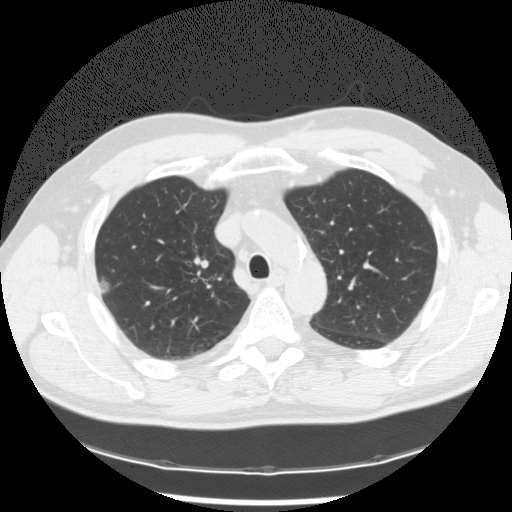
Axial slice from a low-dose chest CT screening exam. First (baseline) screen. Lung window (W 1500 / L -600 HU). 120 kVp. 512 × 512 image matrix. Male, age 62 years at enrolment. Former smoker at enrolment.
Expert reader's lesion annotation, bounding box [x1, y1, x2, y2] px = [88, 271, 116, 301]. The exam's reader record, not a measurement of the box and not confirmed to be the same lesion: non-calcified nodule or mass ≥4 mm, right upper lobe, 14 × 11 mm, poorly defined margins, mixed attenuation. Official screen result: positive, change unspecified: nodule(s) >= 4 mm or enlarging nodule(s), mass(es), or other non-specific abnormalities suspicious for lung cancer. Later outcome: lung cancer diagnosed 343 days after this screen — adenocarcinoma, NOS, right upper lobe, poorly differentiated (G3), stage IIB (AJCC 6th edition), 5 mm at pathology.